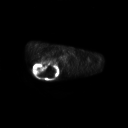
FDG PET of an extremity soft-tissue mass (from a PET/CT study), one axial slice. Position 205 of 267 along the scan axis. 128 × 128 image matrix, field of view 700 × 700 mm. Patient: male, 61 years. Case-level facts recorded for this patient, not image findings: histological type: pleiomorphic spindle cell undifferentiated; grade: high; site of the primary tumour: right parascapusular.
Structures marked on this image (expert contour drawn on MRI and transferred to this co-registered scan by the dataset authors):
- gross tumour volume including surrounding oedema: bounding box (x1, y1, x2, y2) in pixels: (33, 61, 61, 77)
- gross tumour volume (mass): (33, 61, 59, 77)